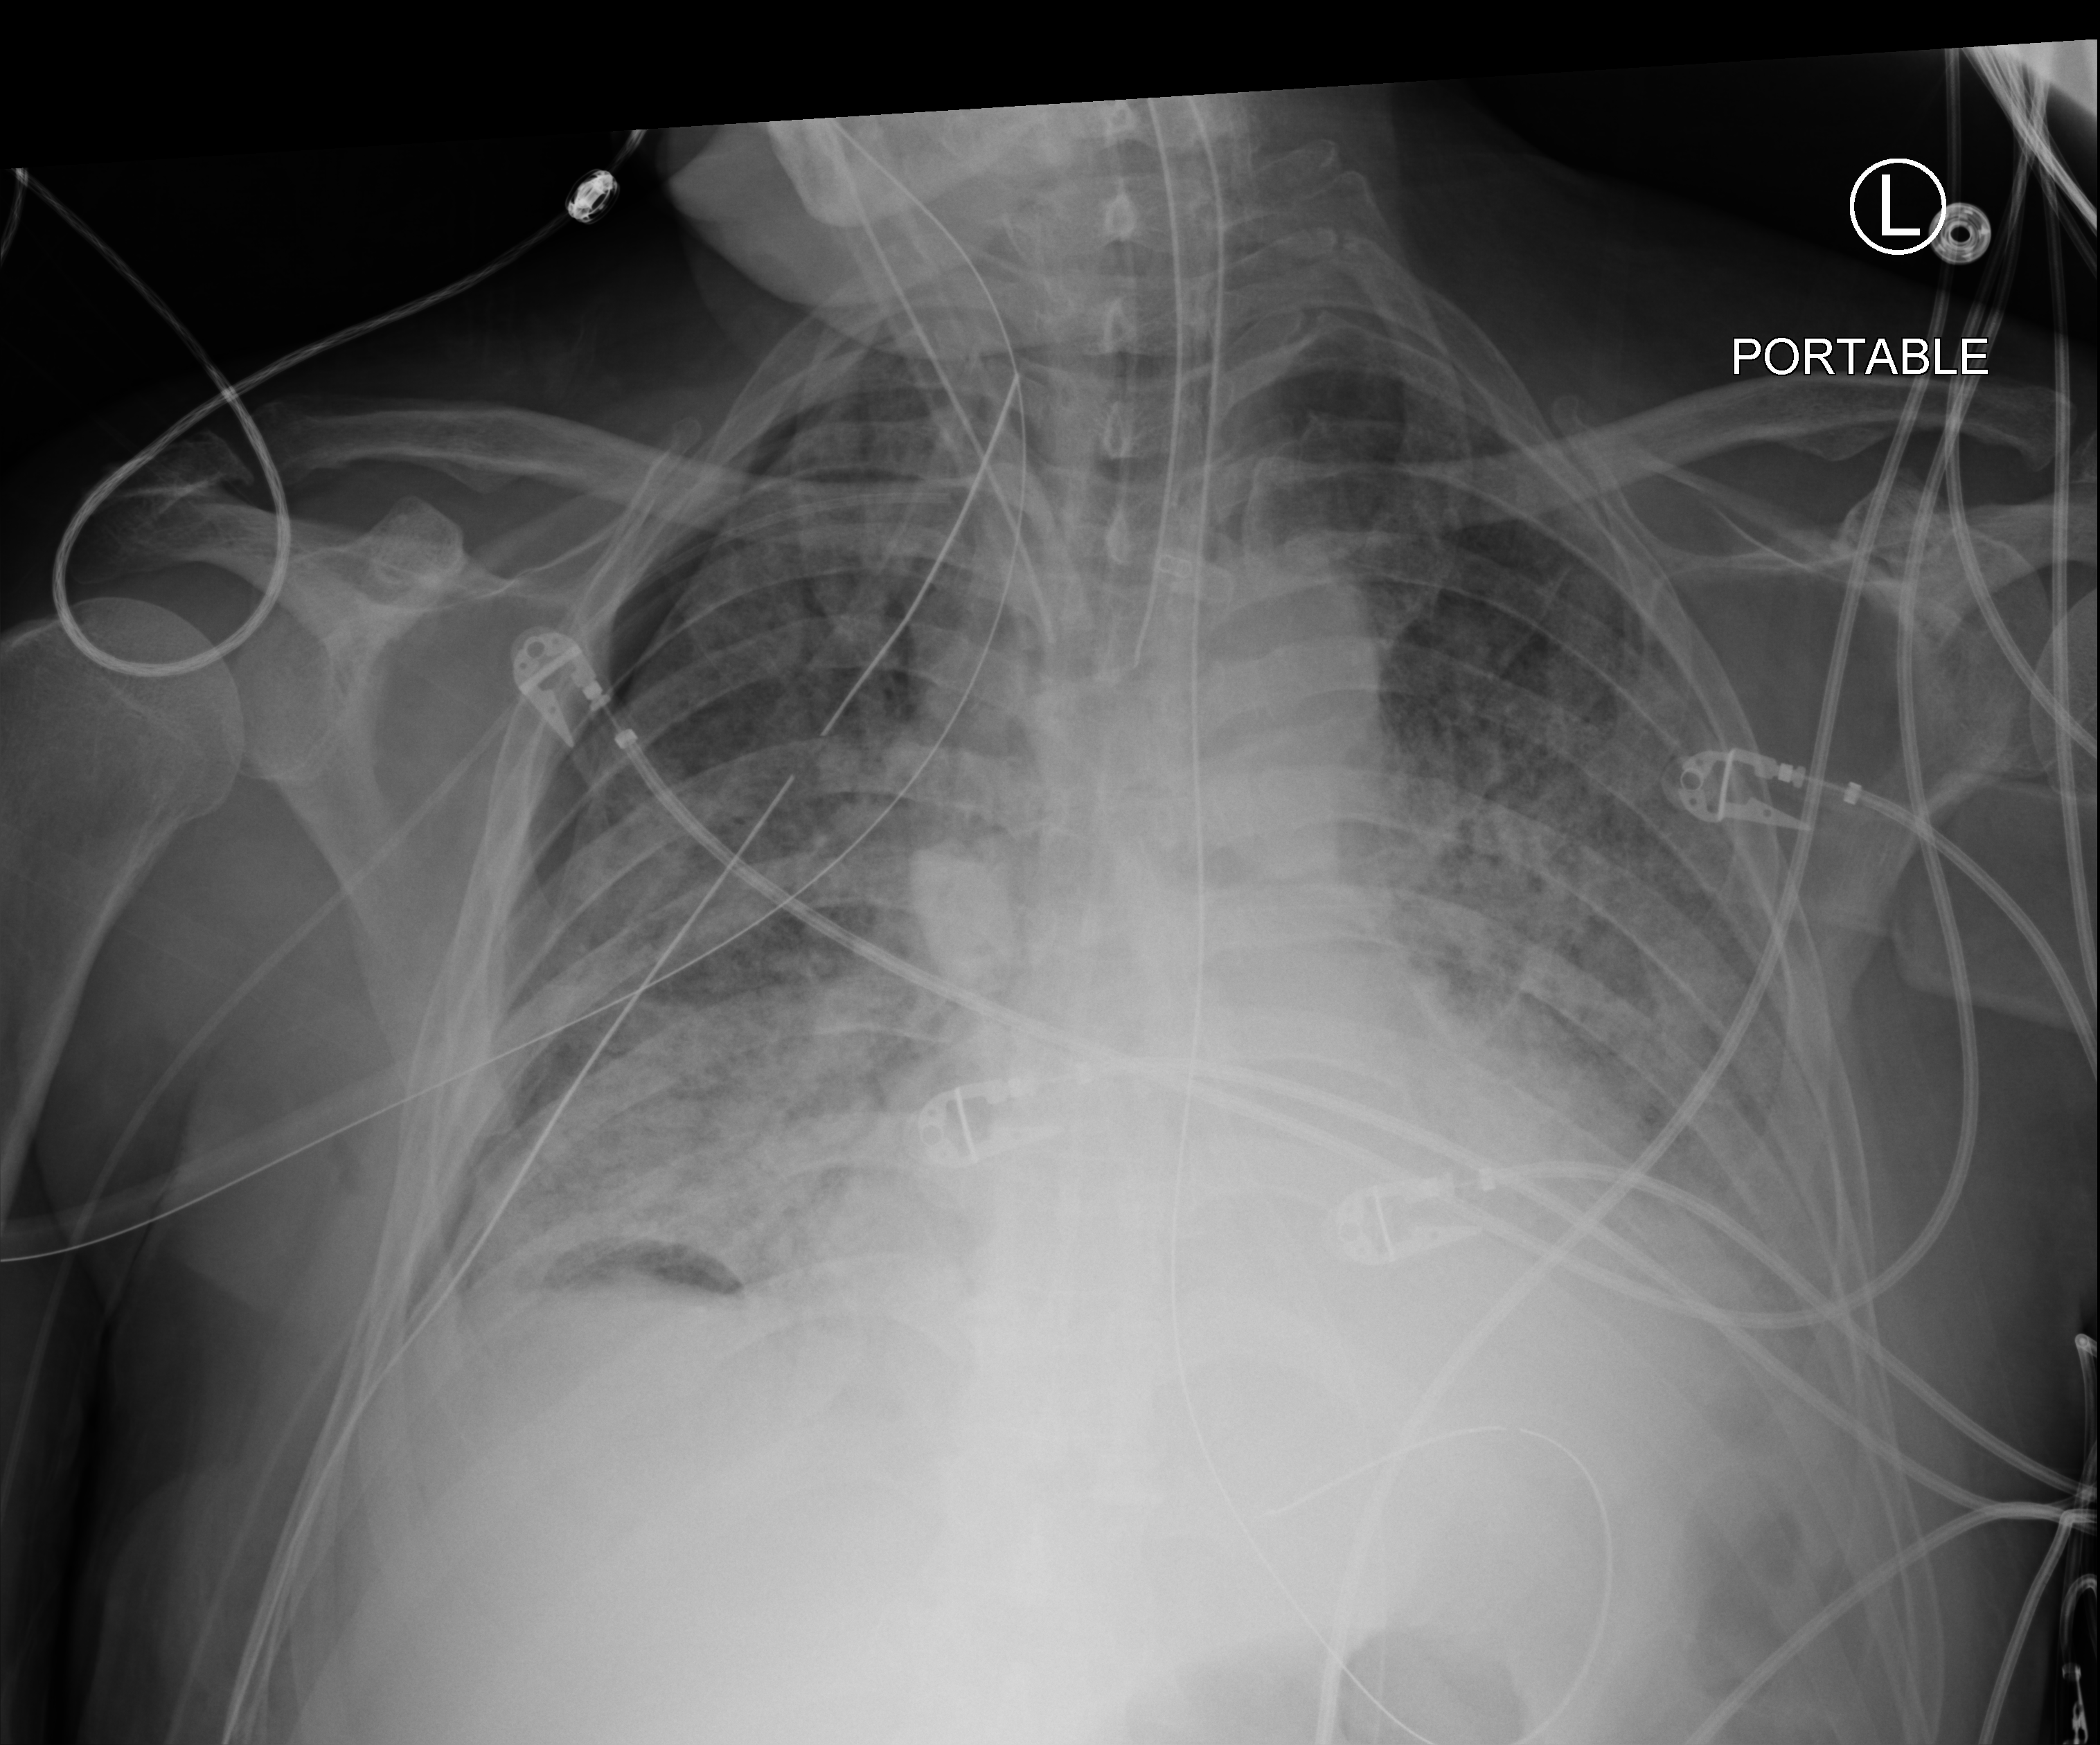
Portable chest radiograph; anteroposterior (AP) projection. Male patient hospitalised with COVID-19, age 60–74 years.
From the hospital-stay record, not from the radiograph (when in the stay this image was taken is not recorded):
- hypertension (admission record): yes
- mechanically ventilated during this hospital stay: yes